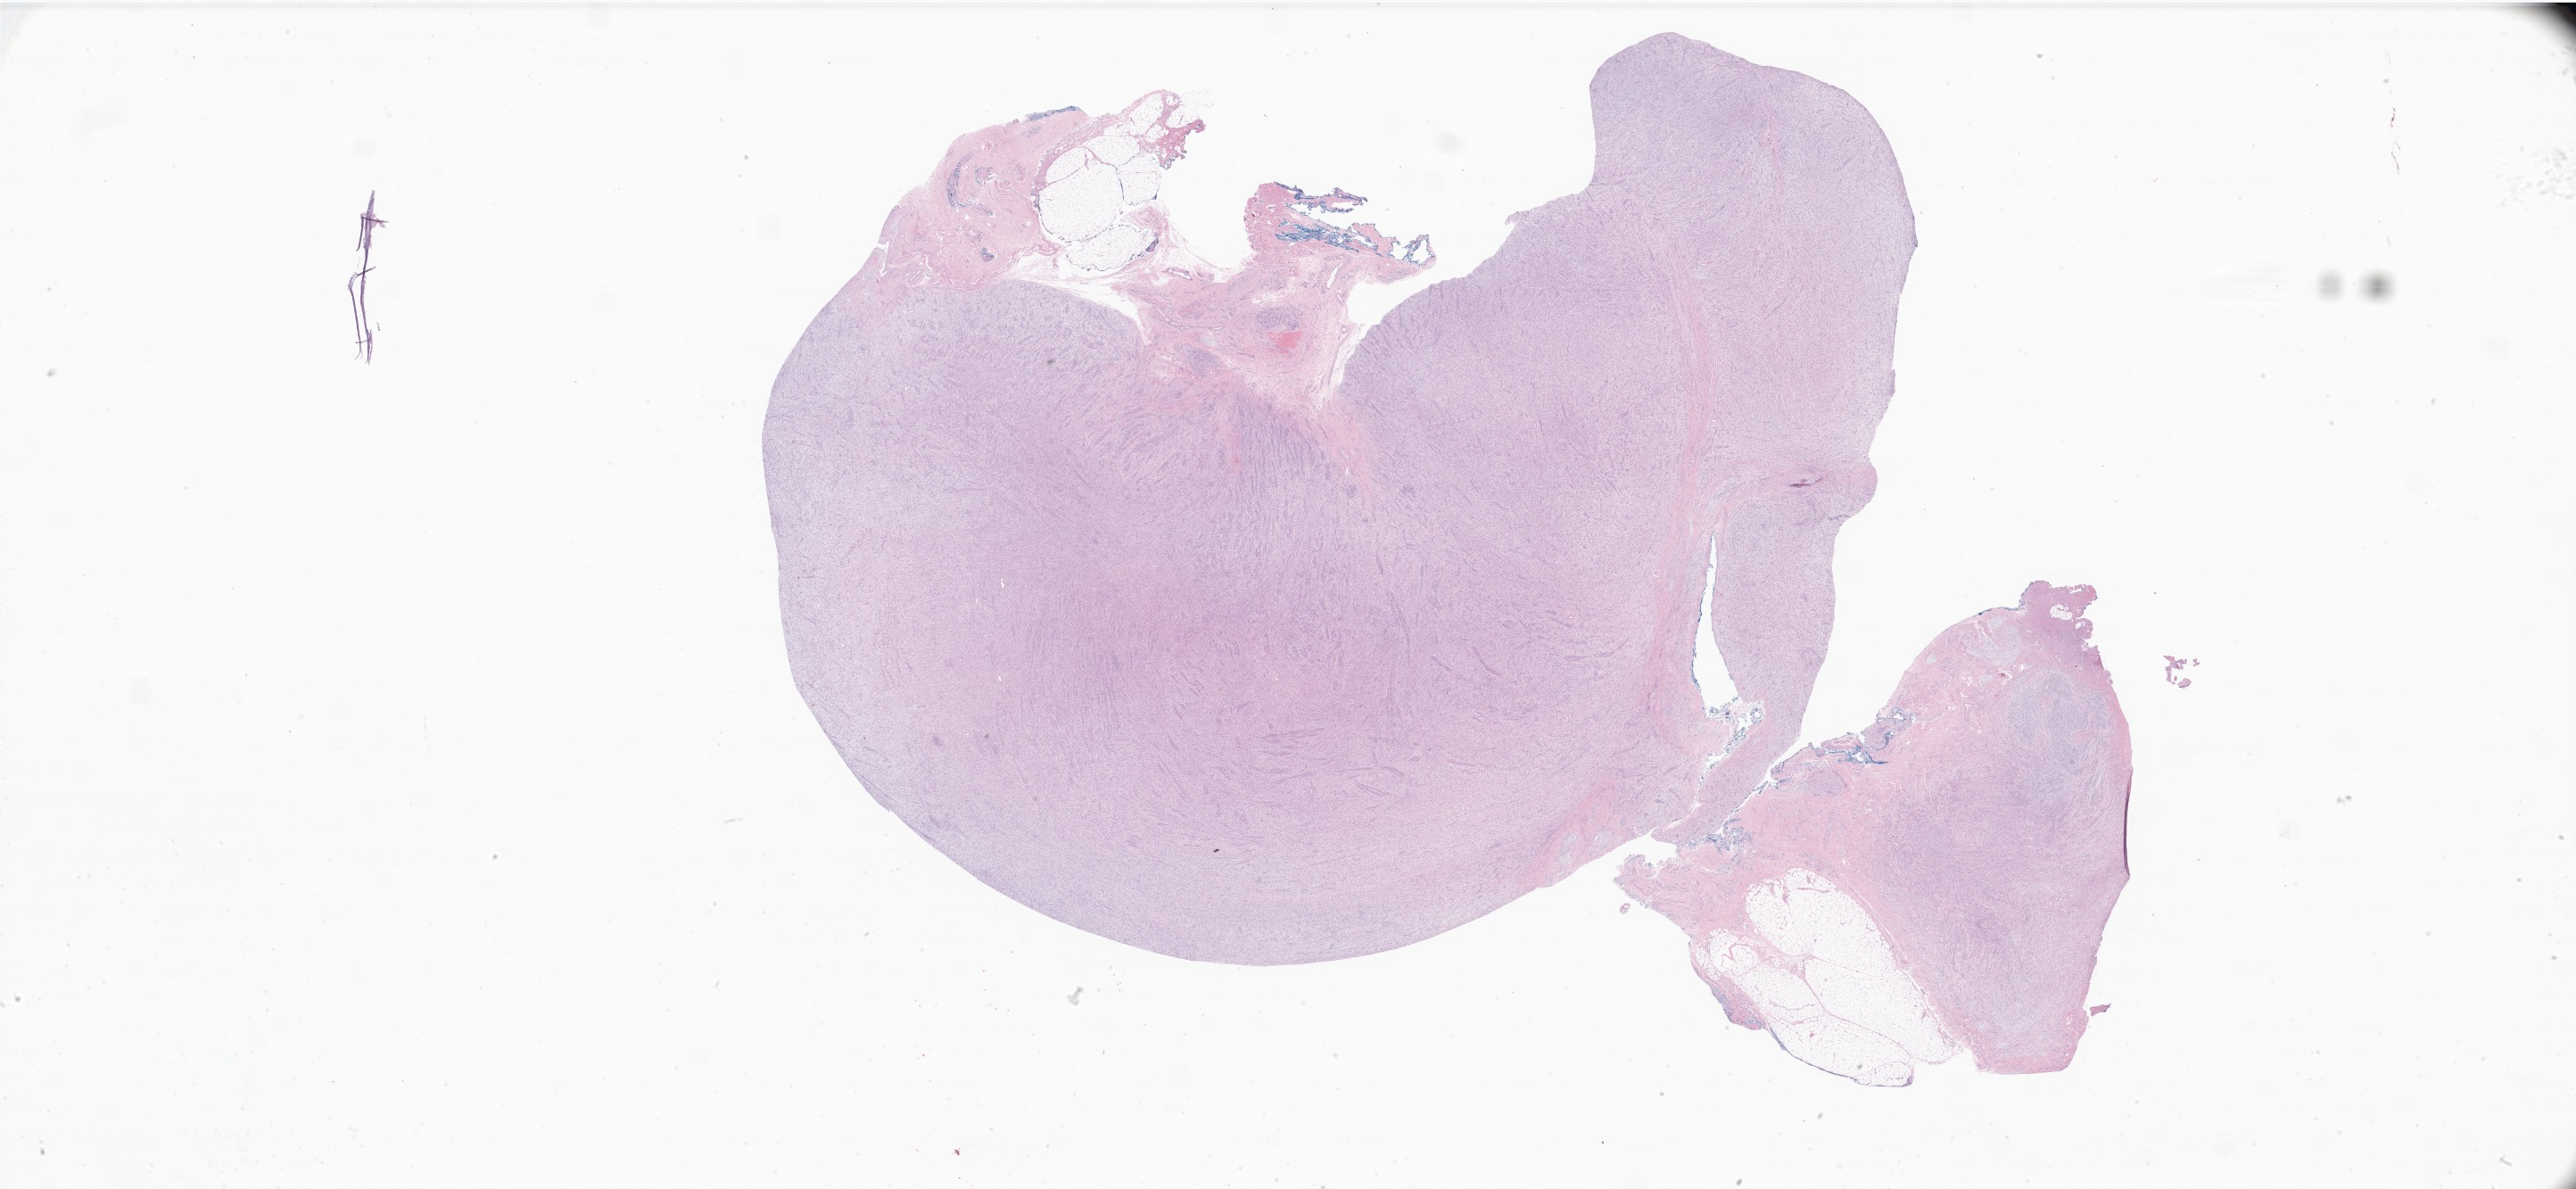
Whole-slide image, haematoxylin and eosin stain of tumor tissue from the soft tissues of head and neck, a low-resolution overview of the entire scanned area, about 48.7 x 22.5 mm; formalin-fixed paraffin-embedded section. Patient: male, age 188 days.
Tissue or organ of origin (case record): connective, subcutaneous and other soft tissues of head, face, and neck. Recorded diagnosis: Rhabdomyosarcoma, NOS.